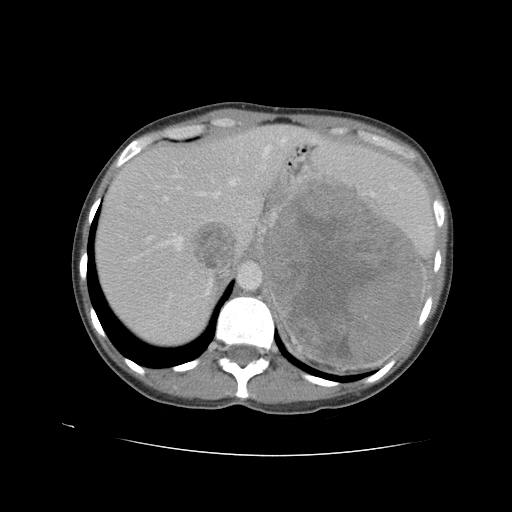
Contrast-enhanced abdominal CT, one axial slice. Position 74 of 90 along the scan axis. Reconstruction kernel STANDARD. 120 kVp. Intravenous contrast given. Soft-tissue window (W 400 / L 40 HU). 5 mm slice thickness. 512 × 512 image matrix, field of view 360 × 360 mm. Female patient. From the clinical record (not read from this slice): diagnosis: adrenocortical carcinoma; tumour side: left adrenal.
Structures marked on this image (semi-automatic segmentation, software-assisted and operator-edited):
- mass: box from (x=266, y=186) to (x=425, y=364) px